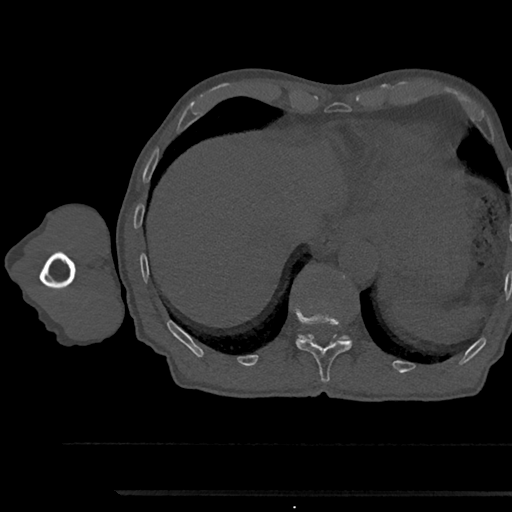
CT including the spine, one axial slice. Position 767 of 797 along the scan axis. Reconstruction kernel Br40s/3. 120 kVp. Bone window (W 1800 / L 400 HU). 512 × 512 image matrix. Patient: male, 79 years. From the clinical record (not read from this slice): primary cancer: prostate.
Outlined on this slice (semi-automatically segmented with operator editing):
- T11 vertebra: box from (x=296, y=315) to (x=352, y=383) px
- T12 vertebra: (x=298, y=334)–(x=349, y=341)